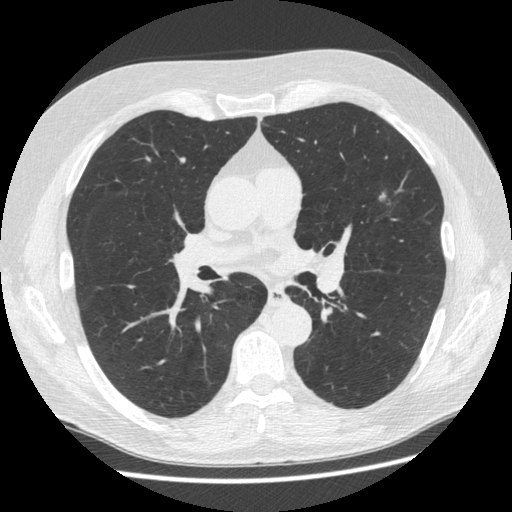
Low-dose screening chest CT, one axial slice. Slice 305 of 545 in the series (ordered by position). Reconstruction kernel STANDARD. 120 kVp. Lung window (W 1500 / L -600 HU). 1.25 mm slice thickness. 512 × 512 image matrix, field of view 360 × 360 mm.
Outlined on this slice (outlined manually by an expert reader):
- lesion 1 (nodule, upper lobe of left lung): bounding box (x1, y1, x2, y2) in pixels: (379, 192, 387, 202)